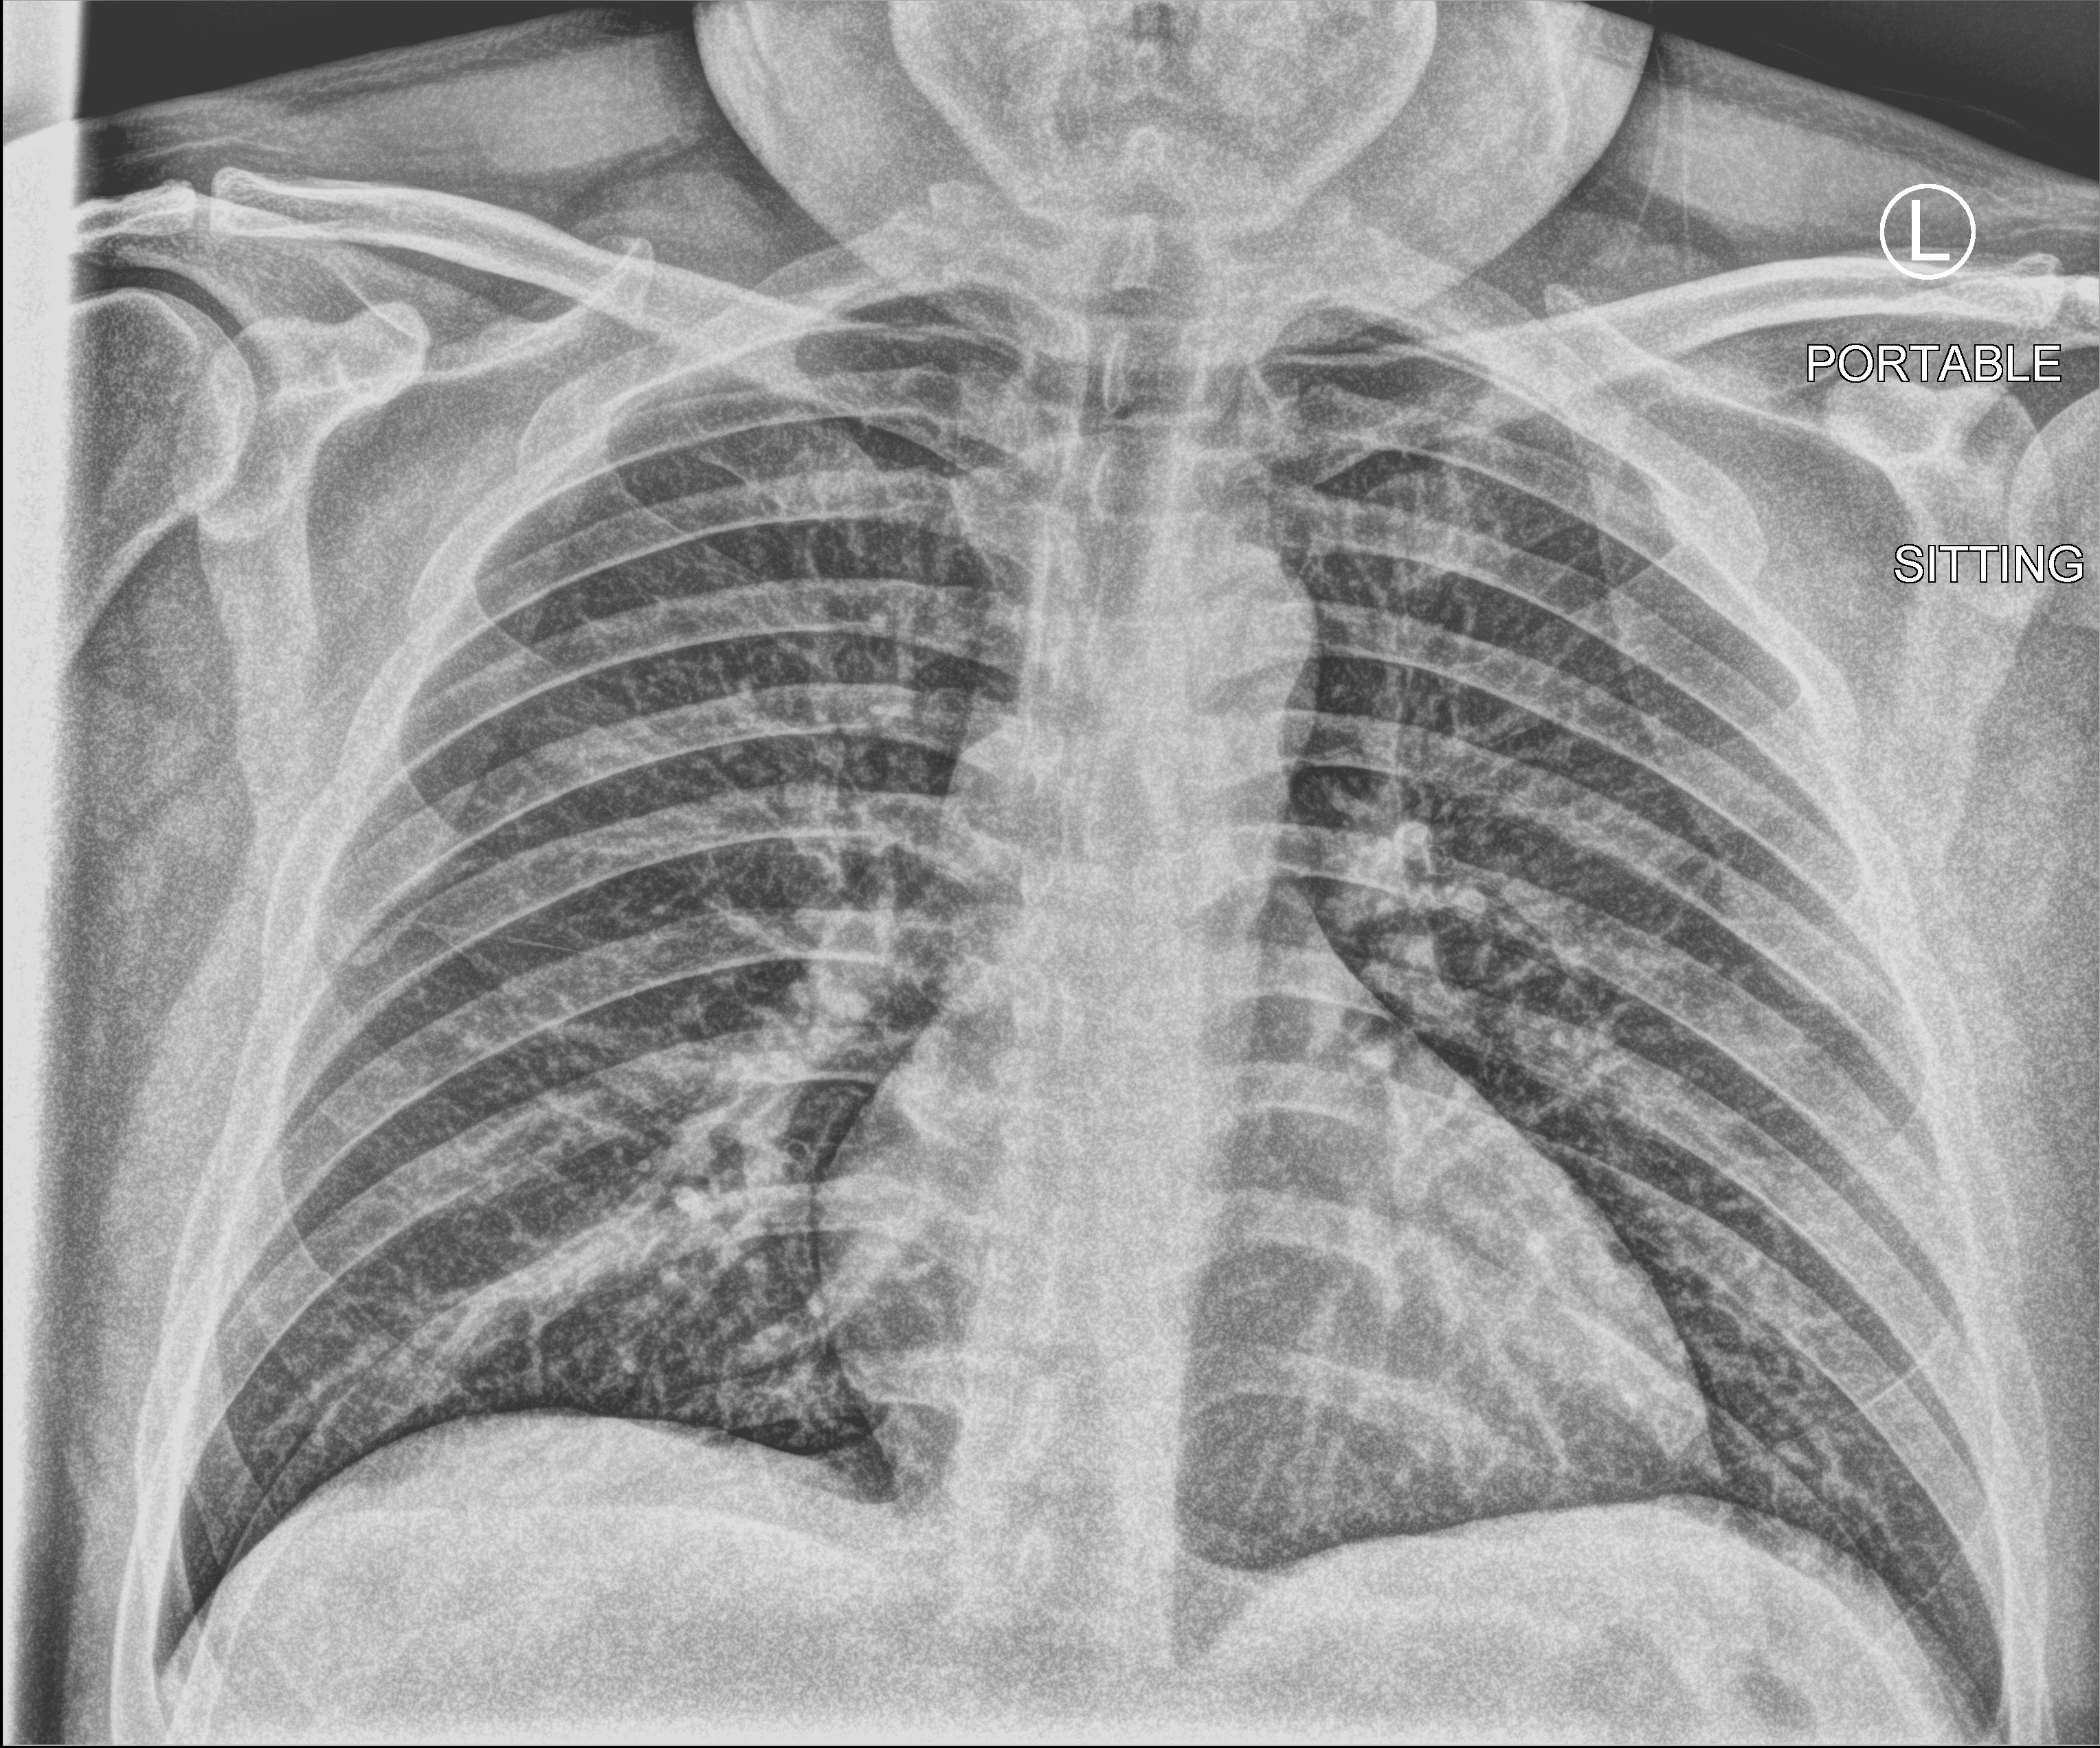
Chest X-ray (portable). Male patient hospitalised with COVID-19, age 18–59 years.
Hospital-stay facts (about this admission, not read from this image; timing relative to this image not recorded):
- admitted to intensive care during this hospital stay: no